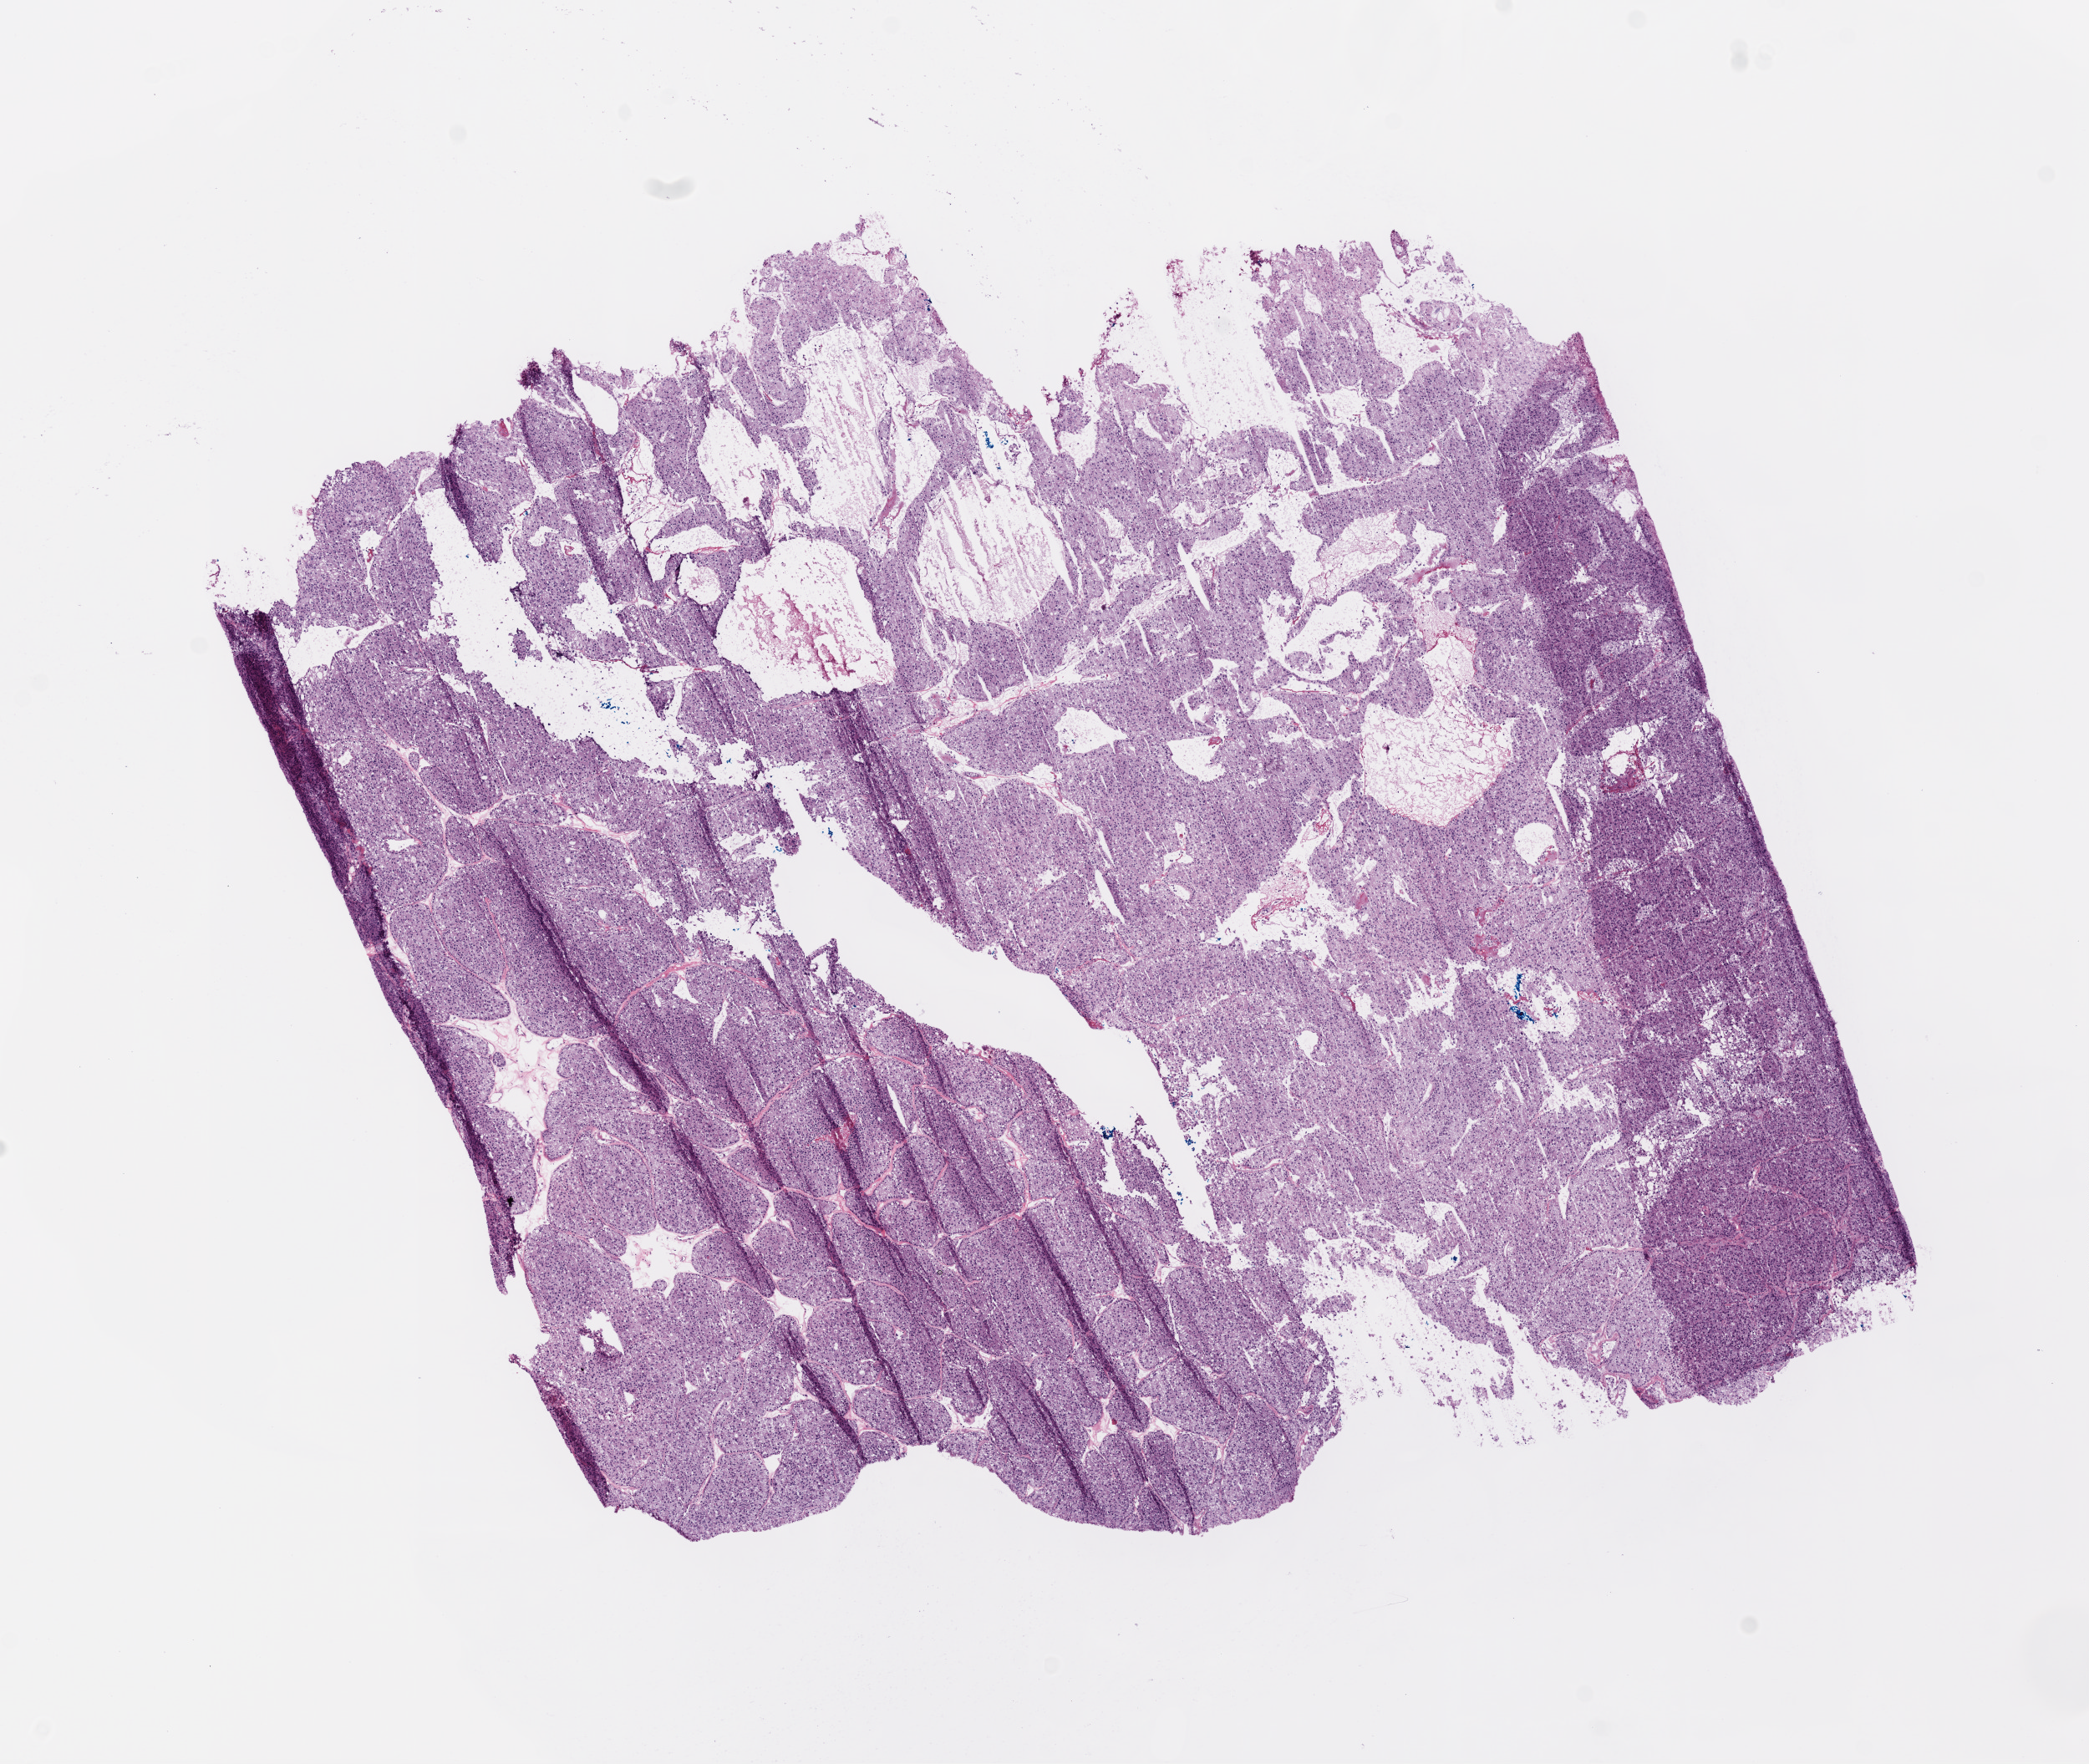
Whole-slide histology image, H&E — a low-resolution overview of the entire scanned area, about 10.0 x 8.5 mm (from a 20x scan), frozen section from the top of the tissue portion, primary tumour sample from the kidney. Male patient; age at initial diagnosis 79 years. Histologic grade: G2 (moderately differentiated). Pathologist review of this section (percent, as recorded): tumour cells 93%, tumour nuclei 90%, normal cells 0%, stromal cells 5%, necrosis 2%.
• AJCC pathologic stage: I
• histologic diagnosis: Clear cell adenocarcinoma, NOS